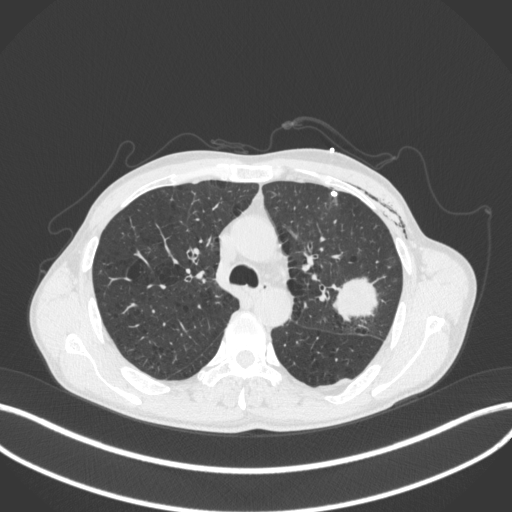
Chest CT, one axial slice; slice 272 of 416 in the series (ordered by position); reconstruction kernel B31f; 120 kVp; lung window (W 1500 / L -600 HU); 1 mm slice thickness; 512 × 512 image matrix, field of view 400 × 400 mm. Male patient, age 58 years. From the clinical record (not read from this slice): clinical TNM (as recorded): T3 N0 M0.
Outlined on this slice (bounding box drawn by a radiologist):
- lung tumour (recorded histology: adenocarcinoma): bounding box <332,271,384,326> (left, top, right, bottom; pixels)